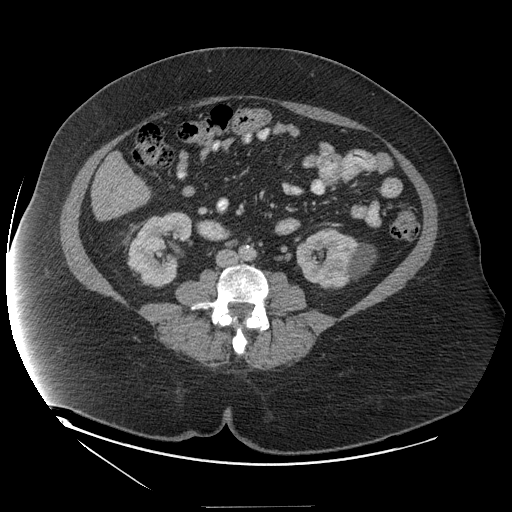
Contrast-enhanced abdominal CT (liver protocol), one axial slice; position 27 of 127 along the scan axis; 140 kVp; soft-tissue window (W 400 / L 40 HU); 2.5 mm slice thickness; 512 × 512 image matrix, field of view 480 × 480 mm. From the clinical record (not read from this slice): diagnosis: hepatocellular carcinoma (patient treated with transarterial chemoembolisation; whether this scan precedes or follows treatment is not stated here); TNM stage (as recorded): Stage-II; Child-Pugh class: A; tumour differentiation: well differentiated.
Outlined on this slice (semi-automatically segmented with operator editing):
- liver parenchyma outside the tumour (the mass and vessels are separate outlines, so this box may not span the whole liver): bounding box (x1, y1, x2, y2) in pixels: (92, 172, 146, 220)